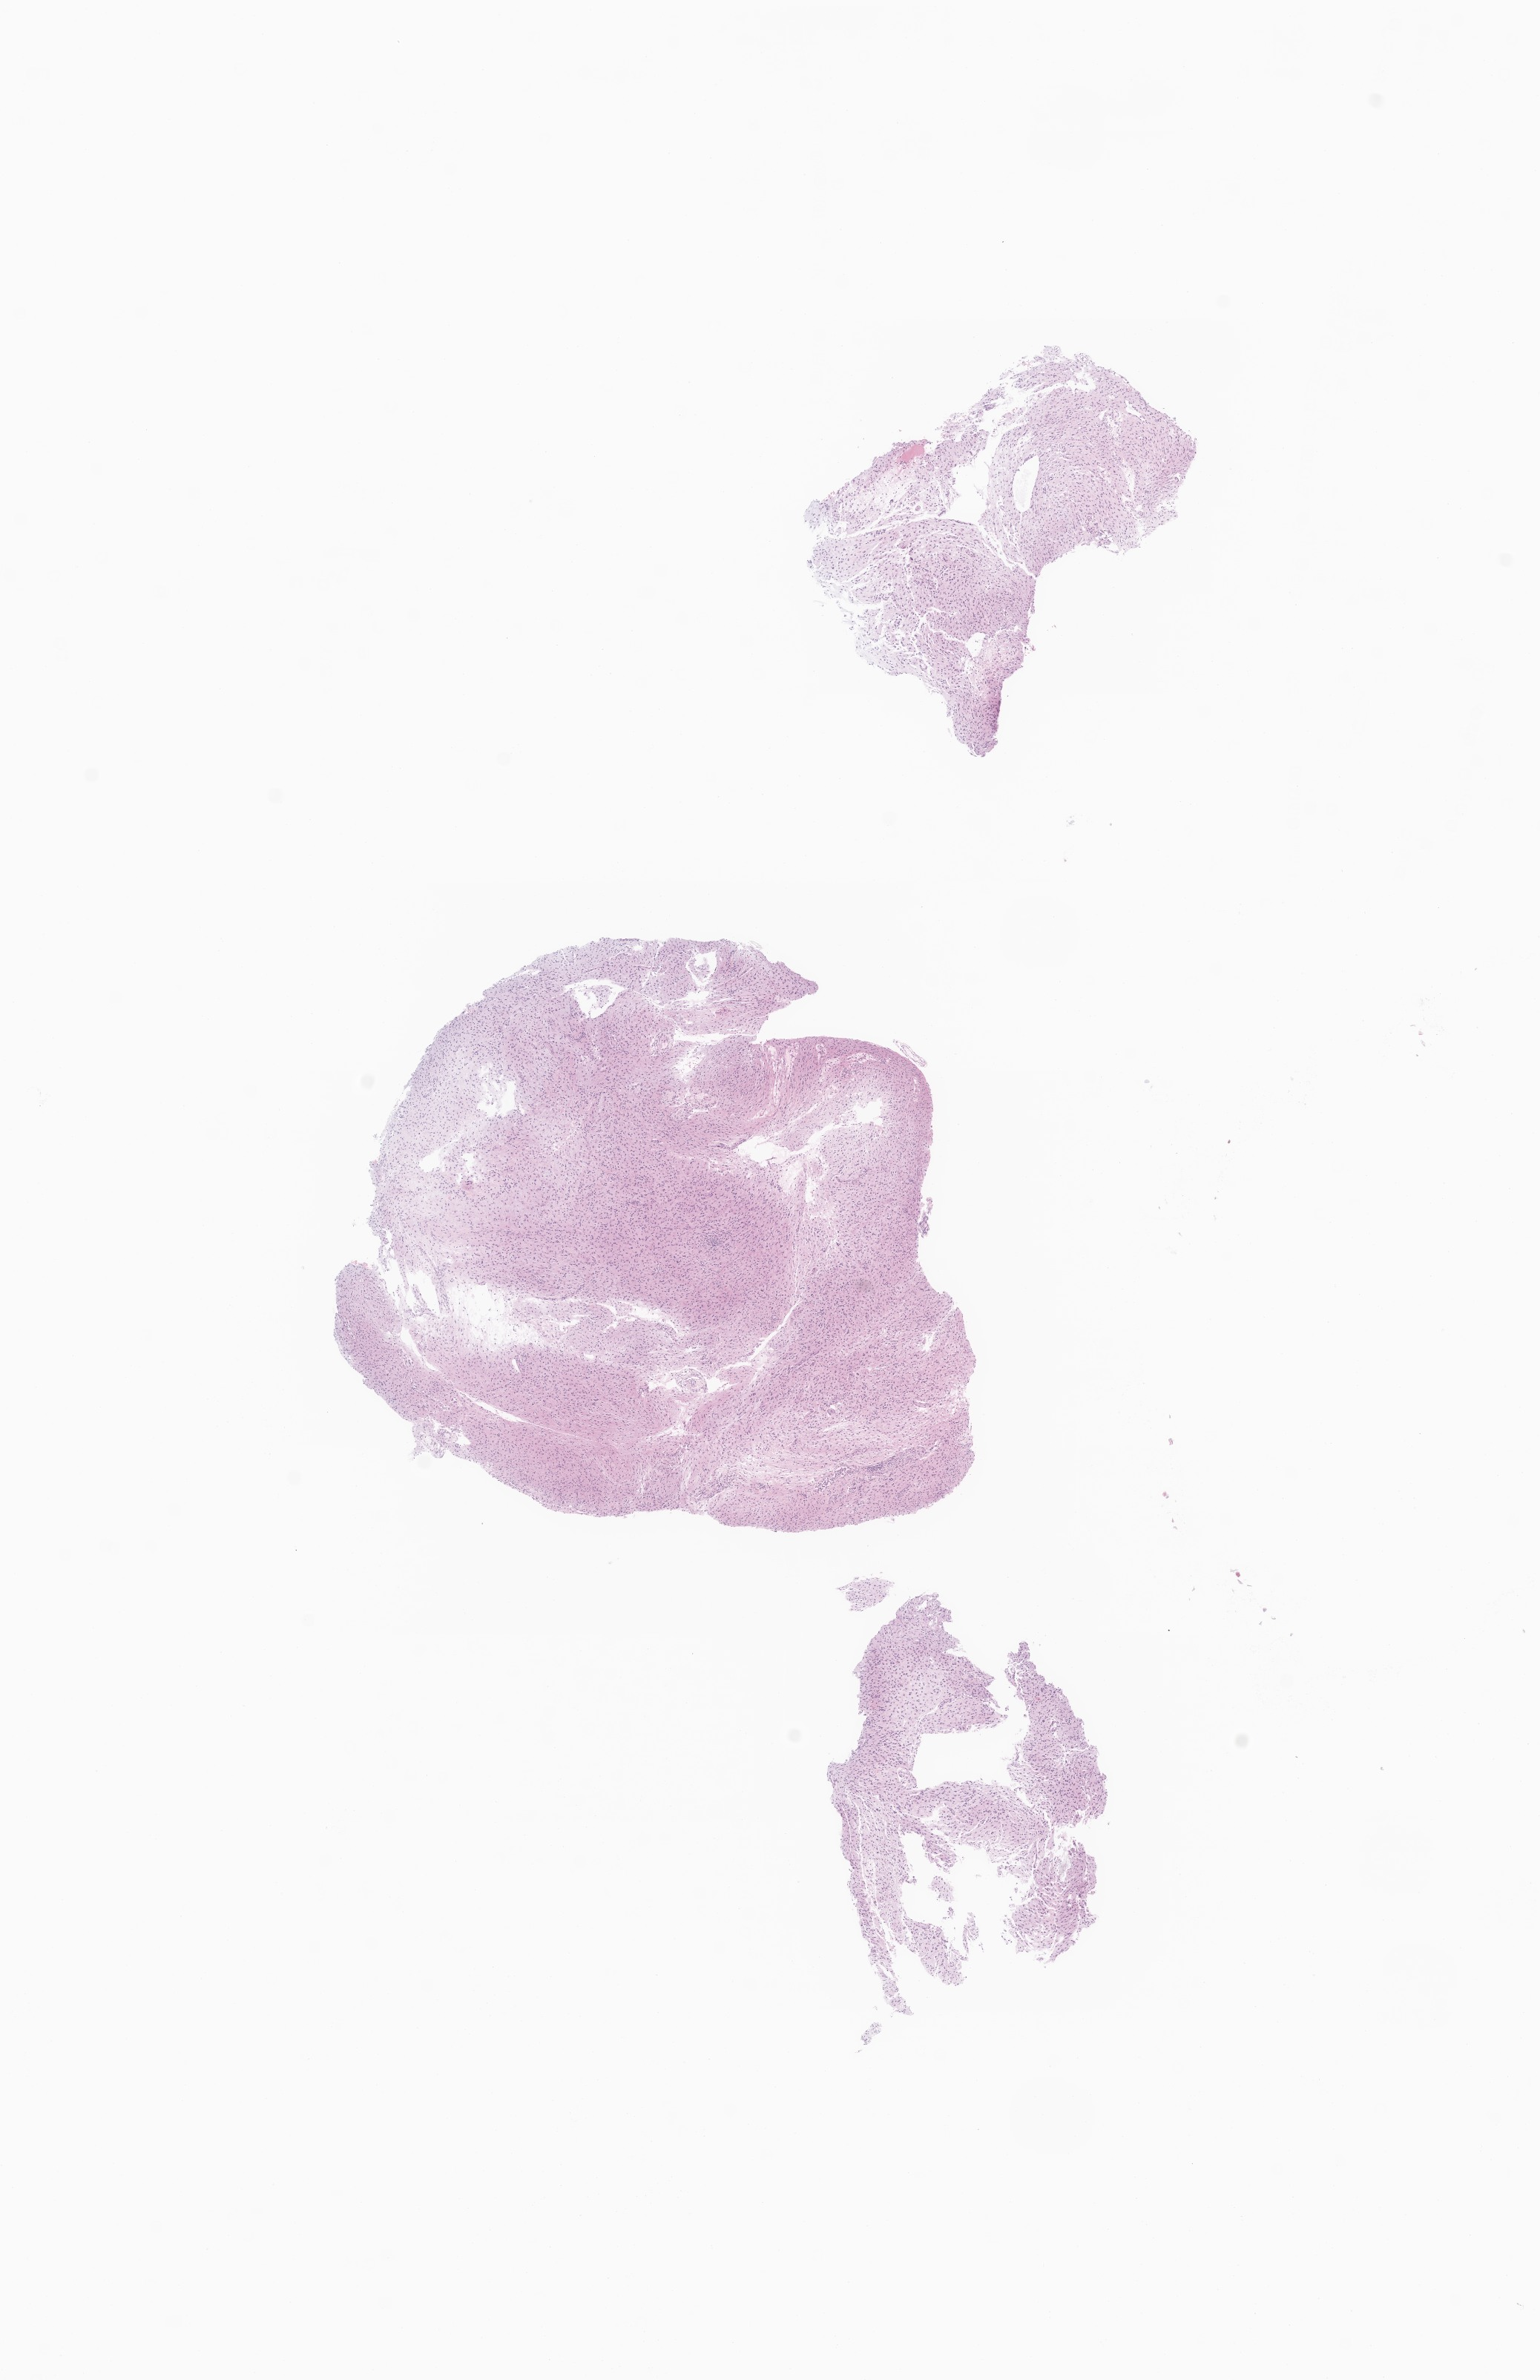
Digitized hematoxylin and eosin (H&E)-stained section of tumor tissue from the brain — low-resolution overview of the scanned area, about 8.8 x 13.5 mm, formalin-fixed, paraffin-embedded (FFPE) tissue. Male patient, age 71 months (5 years 11 months).
• recorded diagnosis: Pilocytic astrocytoma